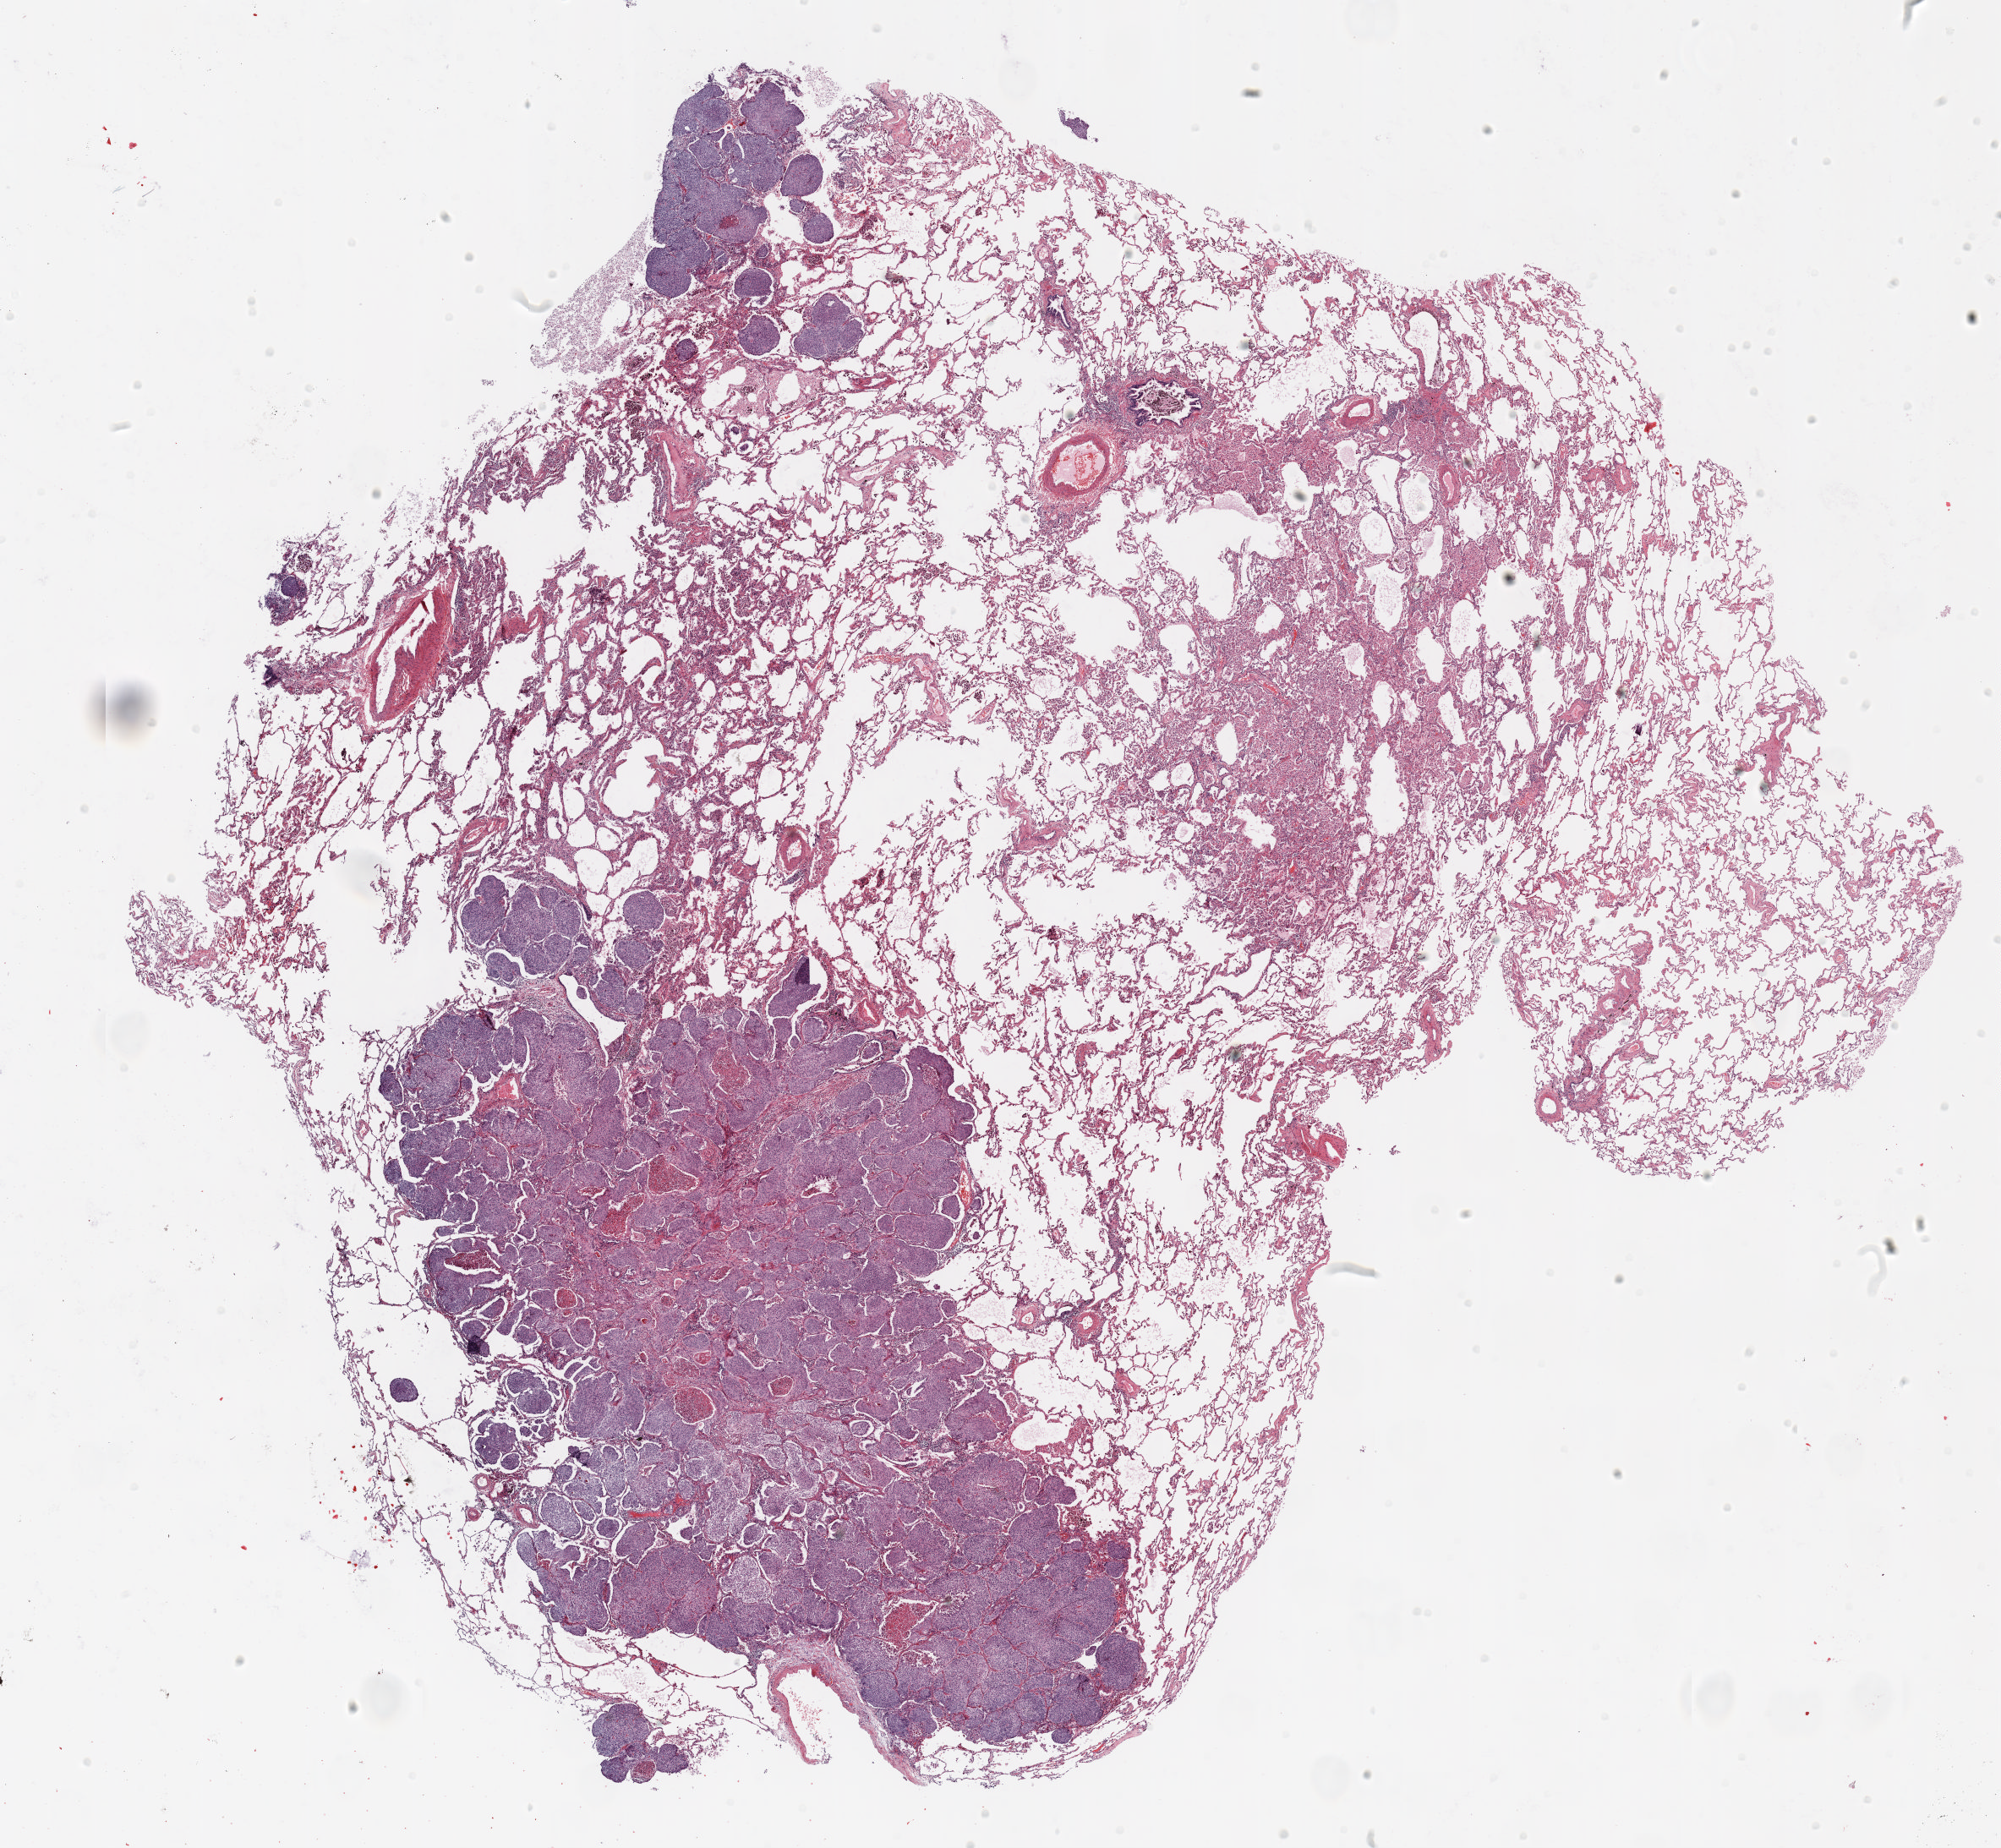
H&E whole-slide image — a low-resolution overview of the entire scanned area, about 19.0 x 17.6 mm (acquisition: 20x scan); FFPE section; lung. Female patient, aged 59 at enrolment. Former smoker at enrolment. Grade: moderately differentiated (G2).
* stage (AJCC 6th edition): IA
* primary tumour location (clinical record): right lower lobe
* participant's lung-cancer diagnosis: Squamous cell carcinoma, NOS
* tumour size (pathology): 13 mm